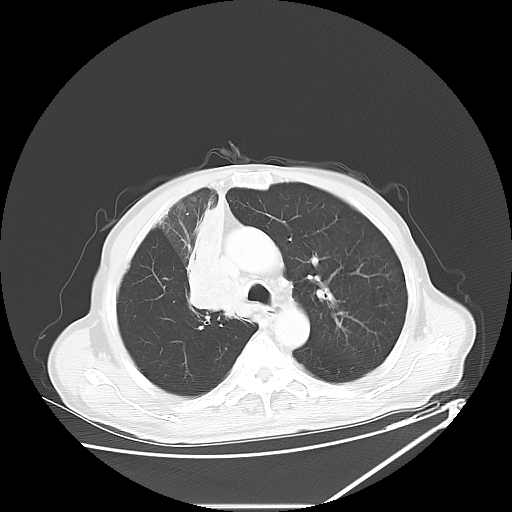
Chest CT, one axial slice; slice 43 of 60 in the series (ordered by position); 120 kVp; lung window (W 1500 / L -600 HU); 5 mm slice thickness; 512 × 512 image matrix. Male patient, age 73 years. From the clinical record (not read from this slice): clinical TNM (as recorded): T2a N1 M0.
Outlined on this slice (rectangle marked by the reading radiologist):
- lung tumour (recorded histology: squamous cell carcinoma): bounding box (x1, y1, x2, y2) in pixels: (179, 195, 246, 319)